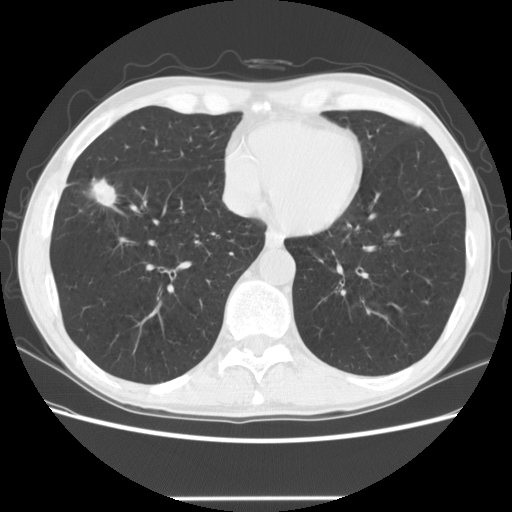
Low-dose screening chest CT, one axial slice. Position 51 of 145 along the scan axis. Reconstruction kernel STANDARD. Lung window (W 1500 / L -600 HU). 2.5 mm slice thickness. 512 × 512 image matrix, field of view 365 × 365 mm.
Outlined on this slice (expert manual segmentation):
- lesion 1 (tumor, middle lobe of right lung): box from (x=89, y=178) to (x=117, y=208) px